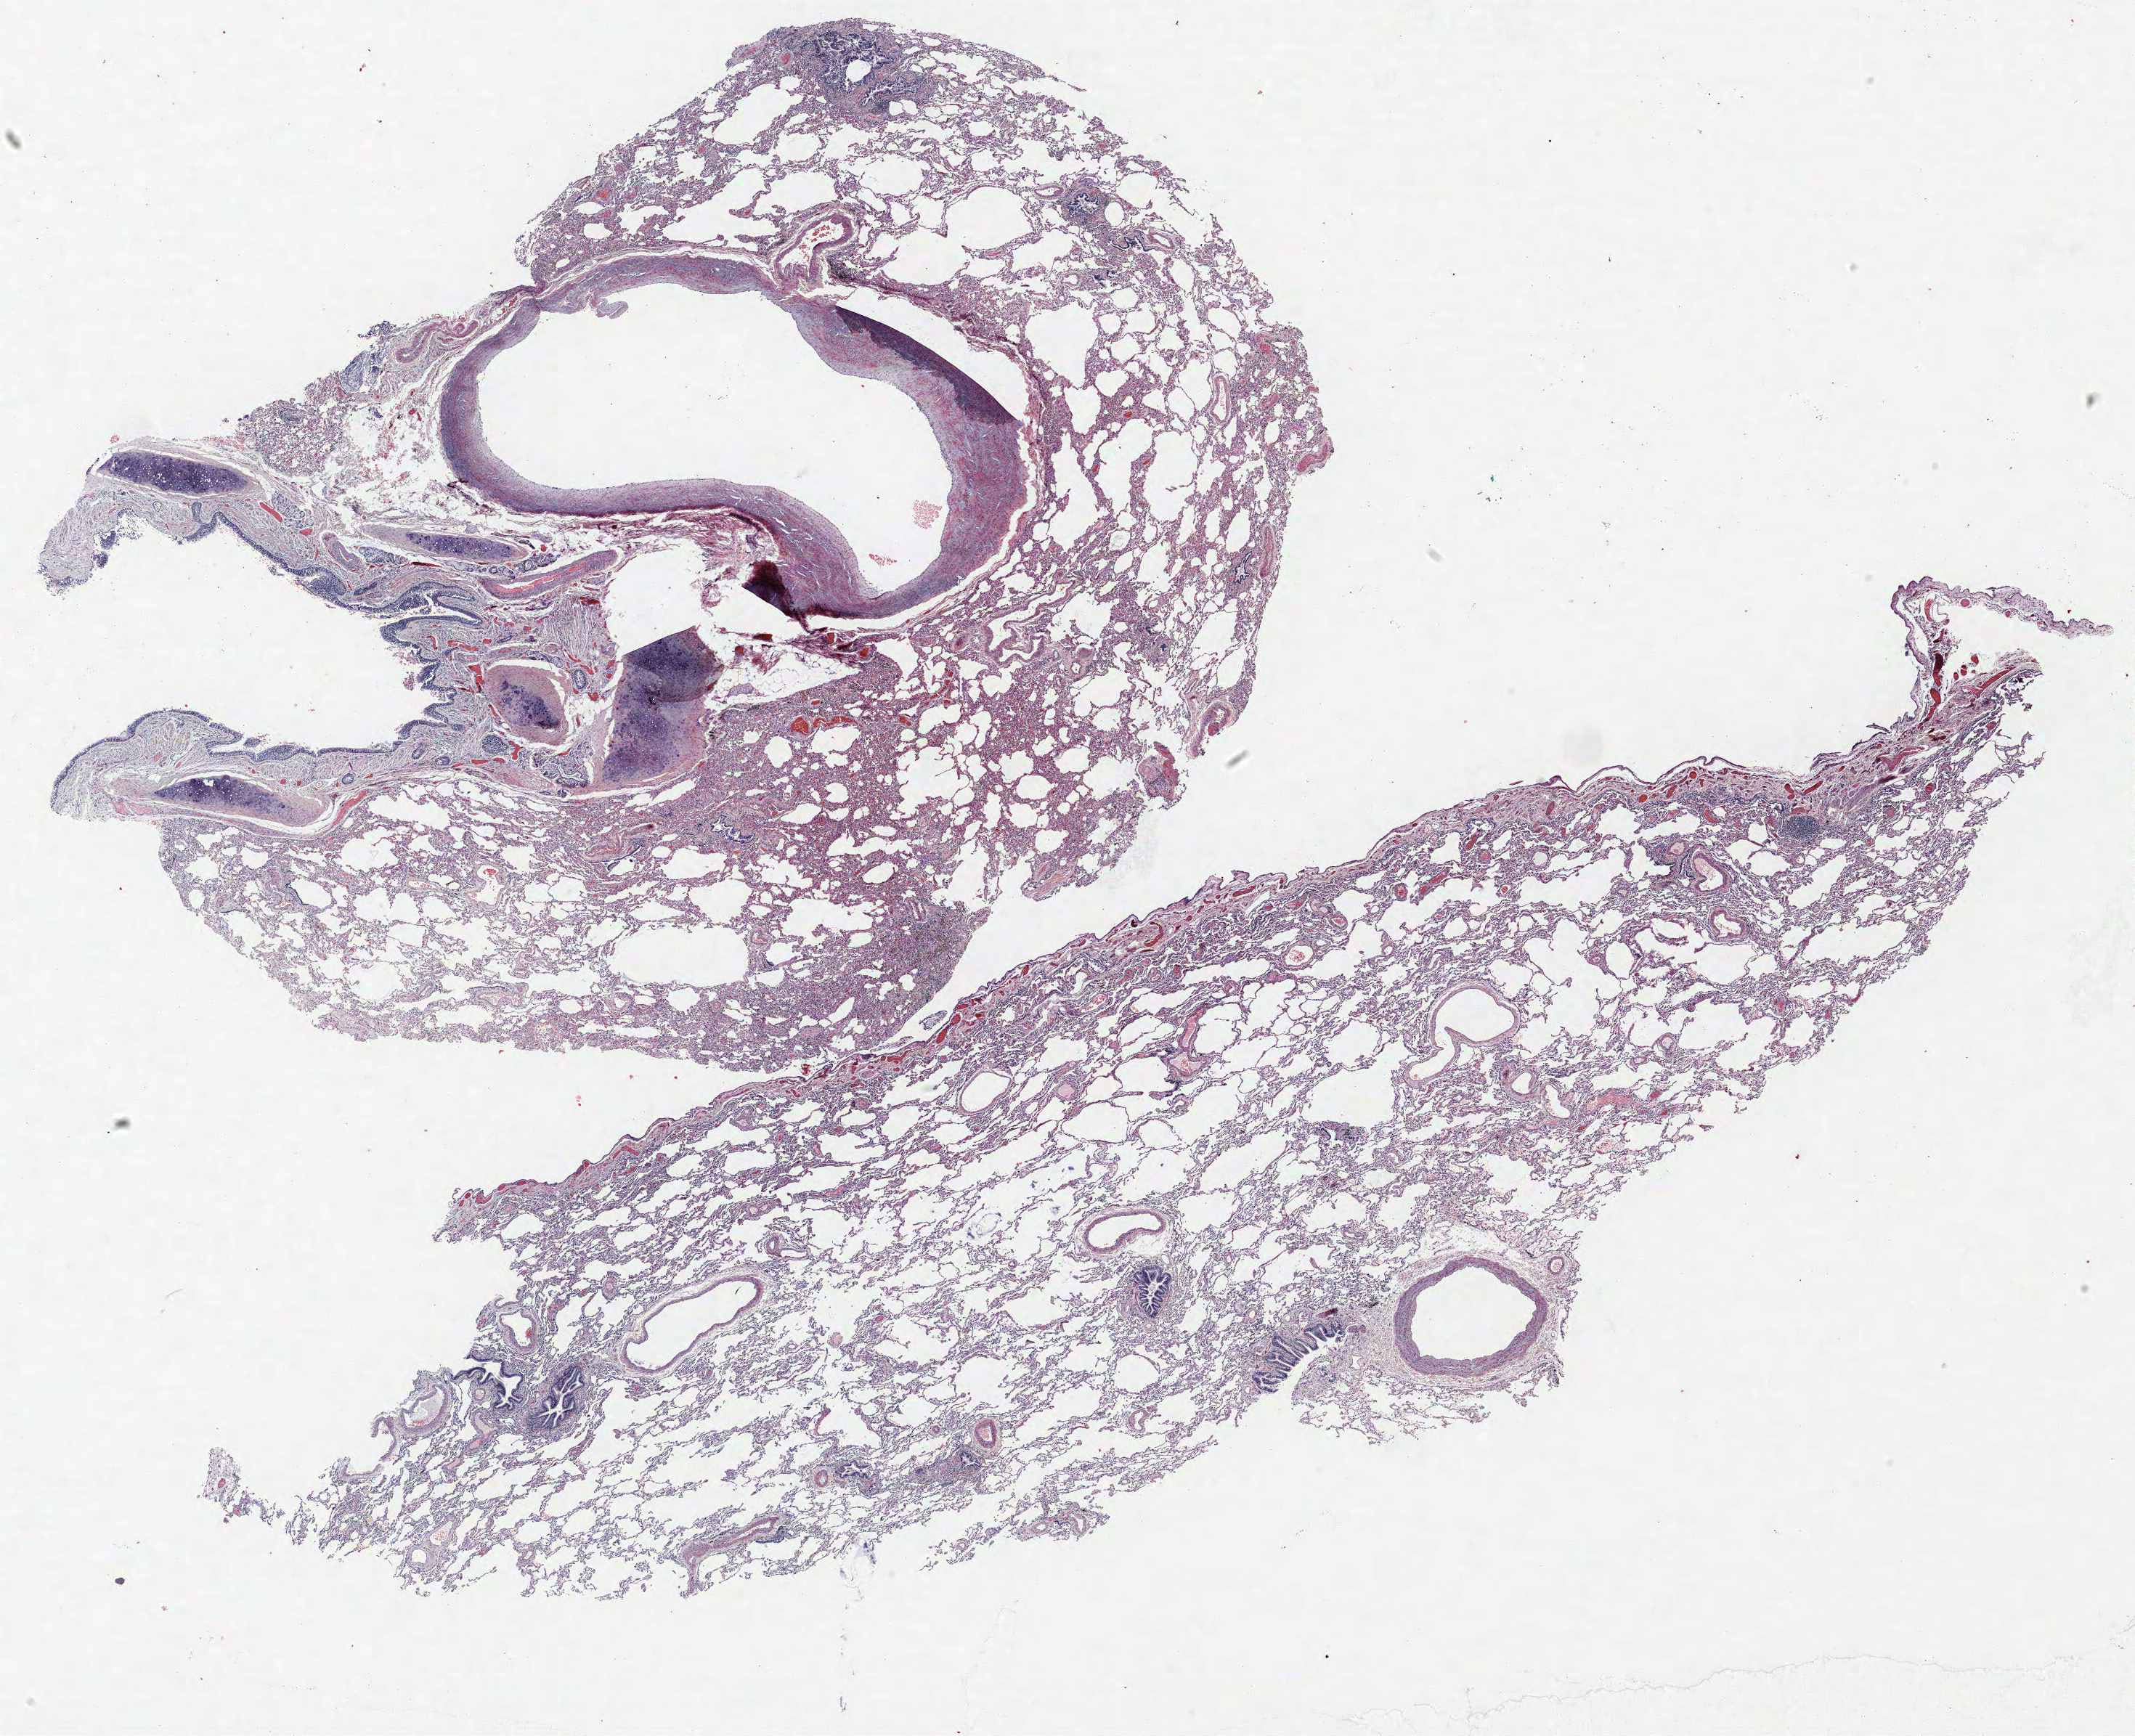
Whole-slide histology image, H&E-stained — a low-resolution overview of the entire scanned area, about 23.5 x 19.1 mm (from a 40x scan), FFPE section, lung tissue. Male patient, aged 69 at enrolment. Current smoker at enrolment. Grade: moderately differentiated (G2).
* participant's lung-cancer diagnosis: Squamous cell carcinoma, NOS
* tumour size (pathology): 23 mm
* stage (AJCC 6th edition): IA
* primary tumour location (clinical record): right lower lobe